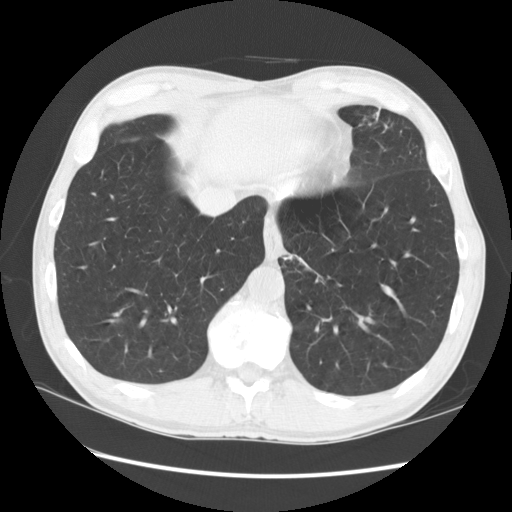
Low-dose screening chest CT, one axial slice. 120 kVp. Lung window (W 1500 / L -600 HU). 2.5 mm slice thickness. 512 × 512 image matrix, field of view 360 × 360 mm.
Structures marked on this image (outlined manually by an expert reader):
- lesion 1 (tumor, lower lobe of left lung): bounding box (x1, y1, x2, y2) in pixels: (373, 111, 378, 122)